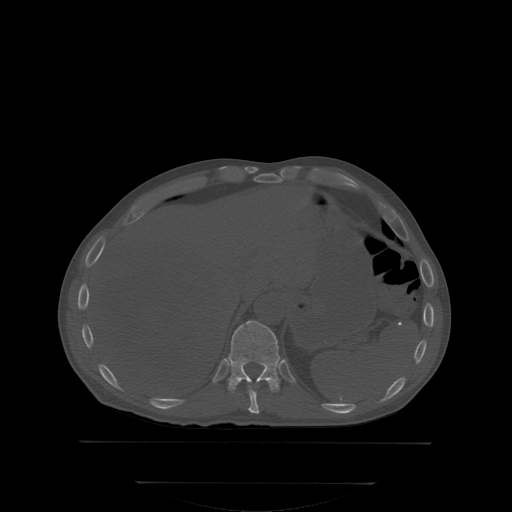
CT including the spine, one axial slice. Bone window (W 1800 / L 400 HU). 512 × 512 image matrix, field of view 500 × 500 mm. Patient: male, 58 years. From the clinical record (not read from this slice): primary cancer: prostate; vertebrae with lytic lesions (as recorded): L1.
Outlined on this slice (semi-automatically segmented with operator editing):
- T10 vertebra: bounding box [x1, y1, x2, y2] px = [248, 387, 259, 413]
- T11 vertebra: [227, 320, 280, 392]